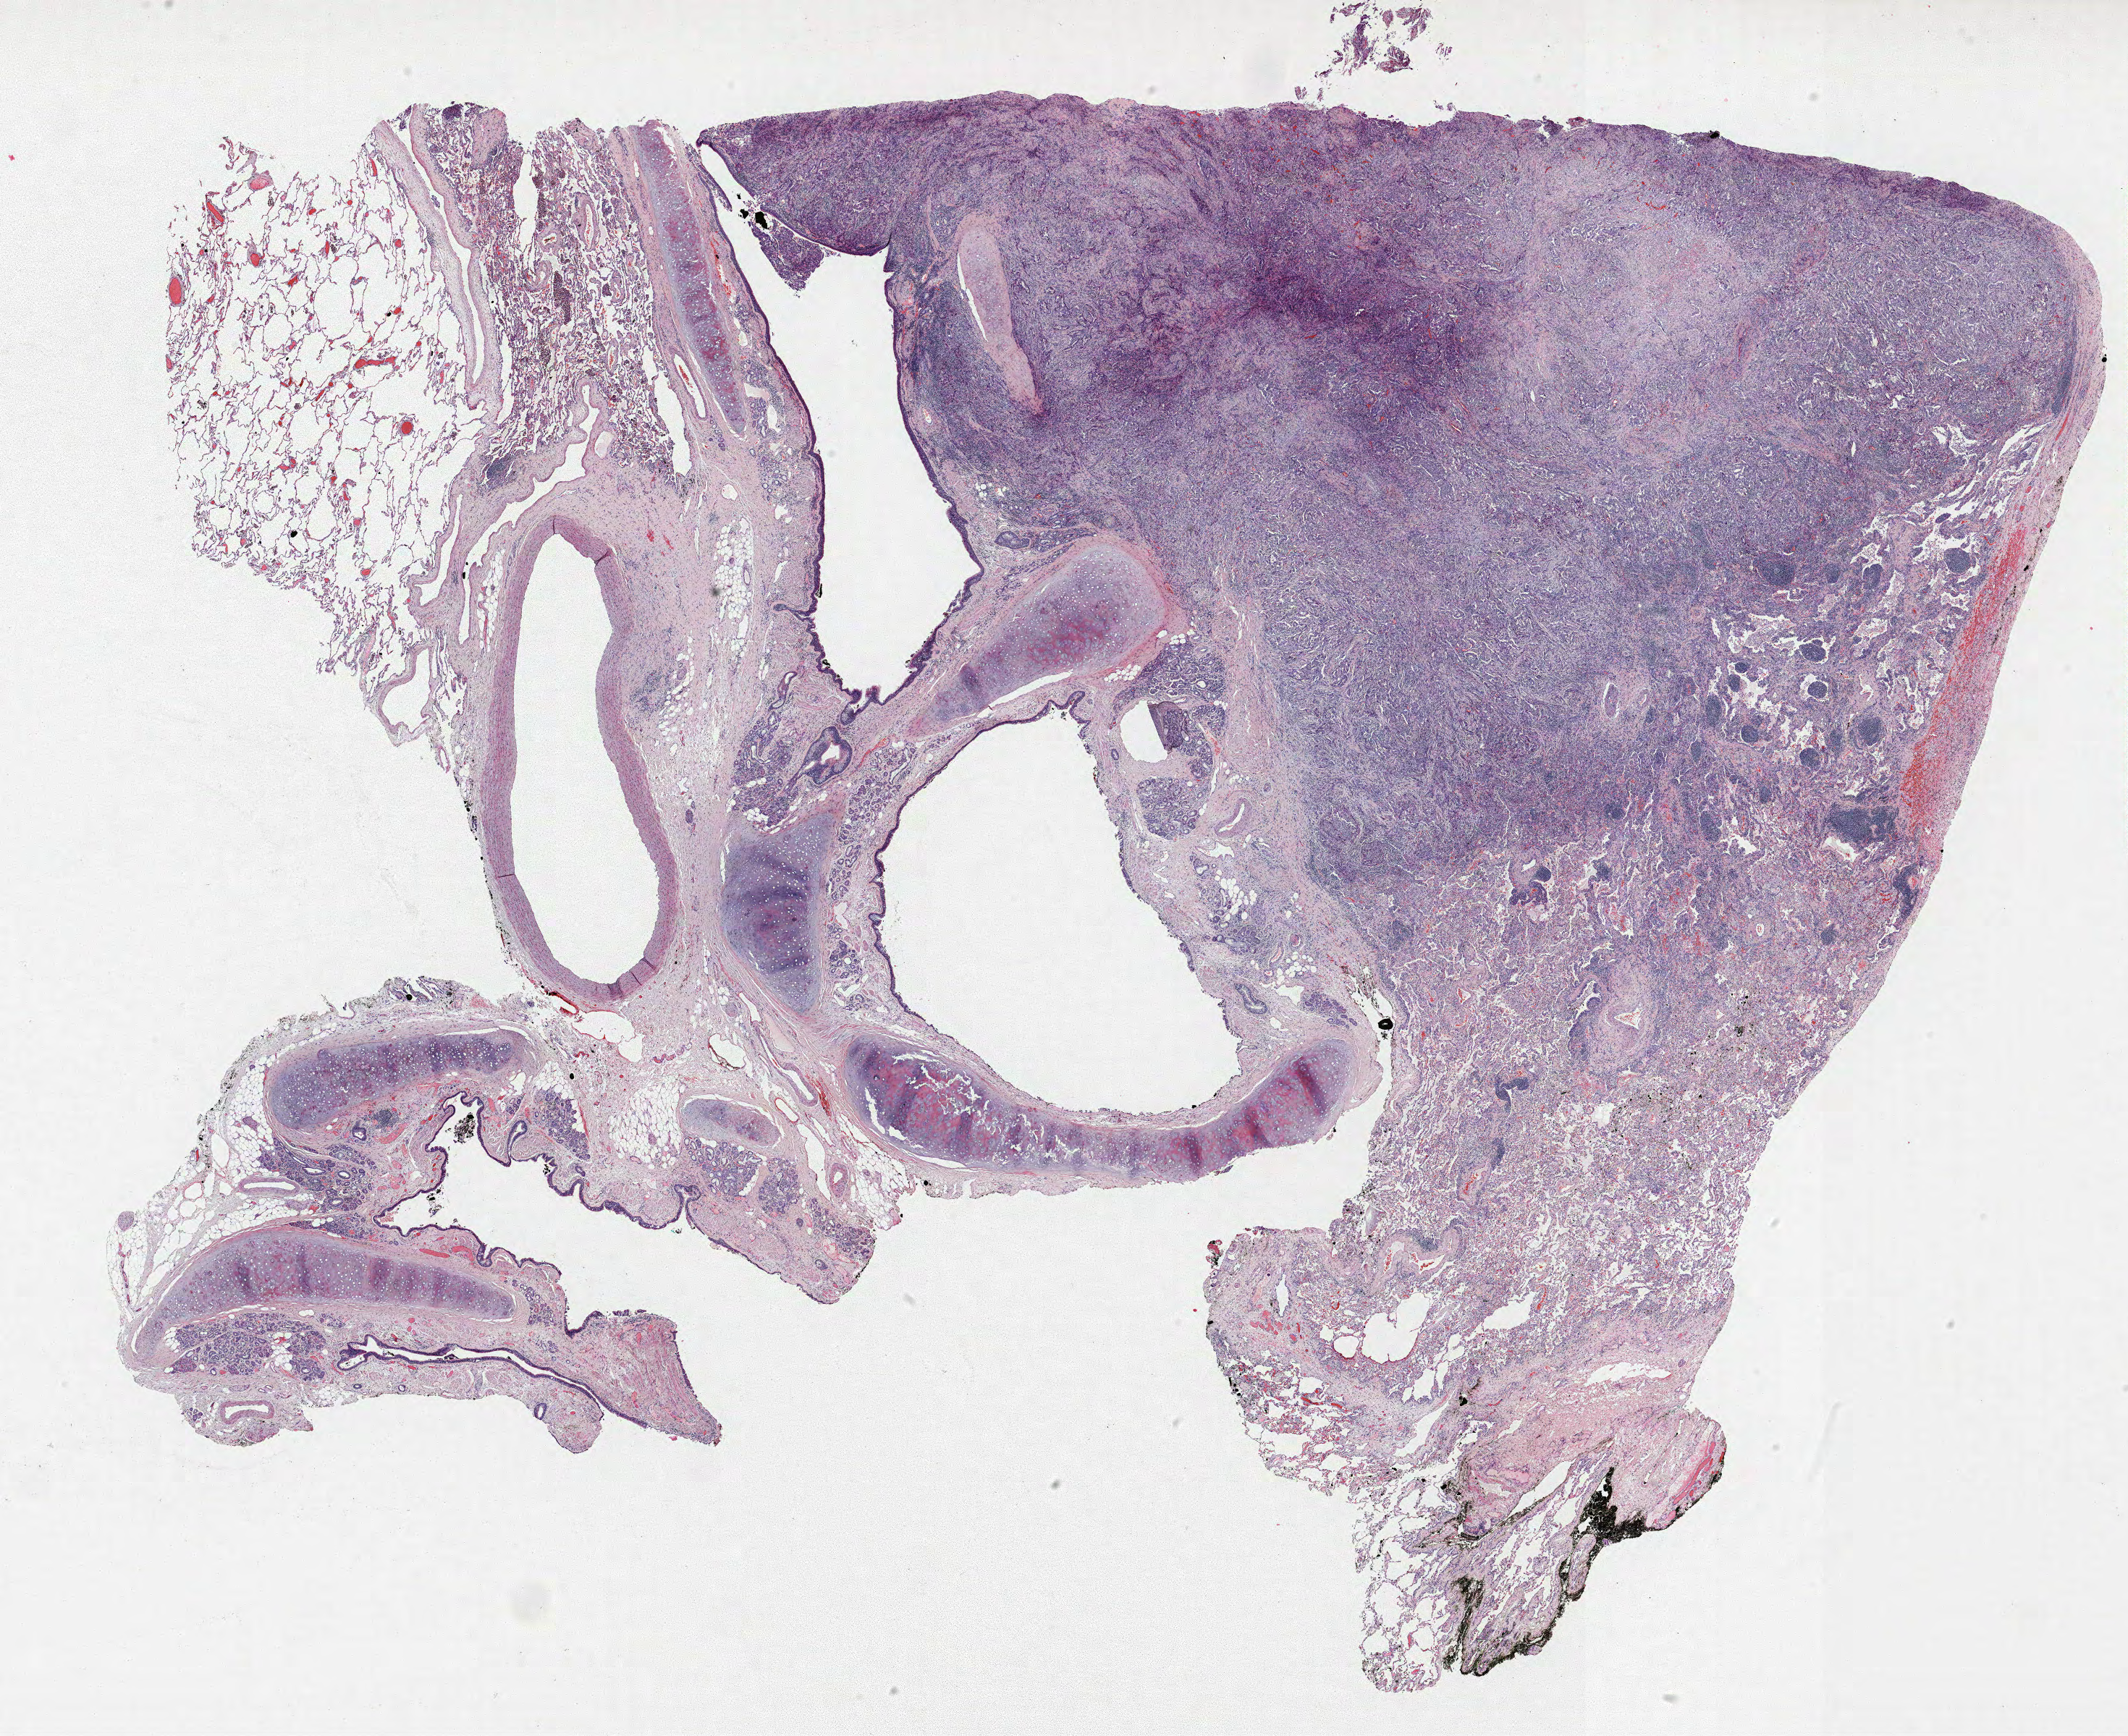
Hematoxylin and eosin (H&E) stained whole-slide image, a low-resolution overview of the entire scanned area, about 23.5 x 19.2 mm (from a 40x scan), formalin-fixed paraffin-embedded (FFPE) section, lung tissue. Male, age 64 at enrolment. Grade: poorly differentiated (G3).
Stage (AJCC 6th edition): IA. Tumour size (pathology): 5 mm. Primary tumour location (clinical record): right upper lobe. ICD-O-3 topography: upper lobe of lung (C34.1). Participant's lung-cancer diagnosis: Bronchiolo-alveolar adenocarcinoma, NOS (ICD-O-3 8250/3). Note: participant had 2 primary lung cancers recorded; fields above describe the first.